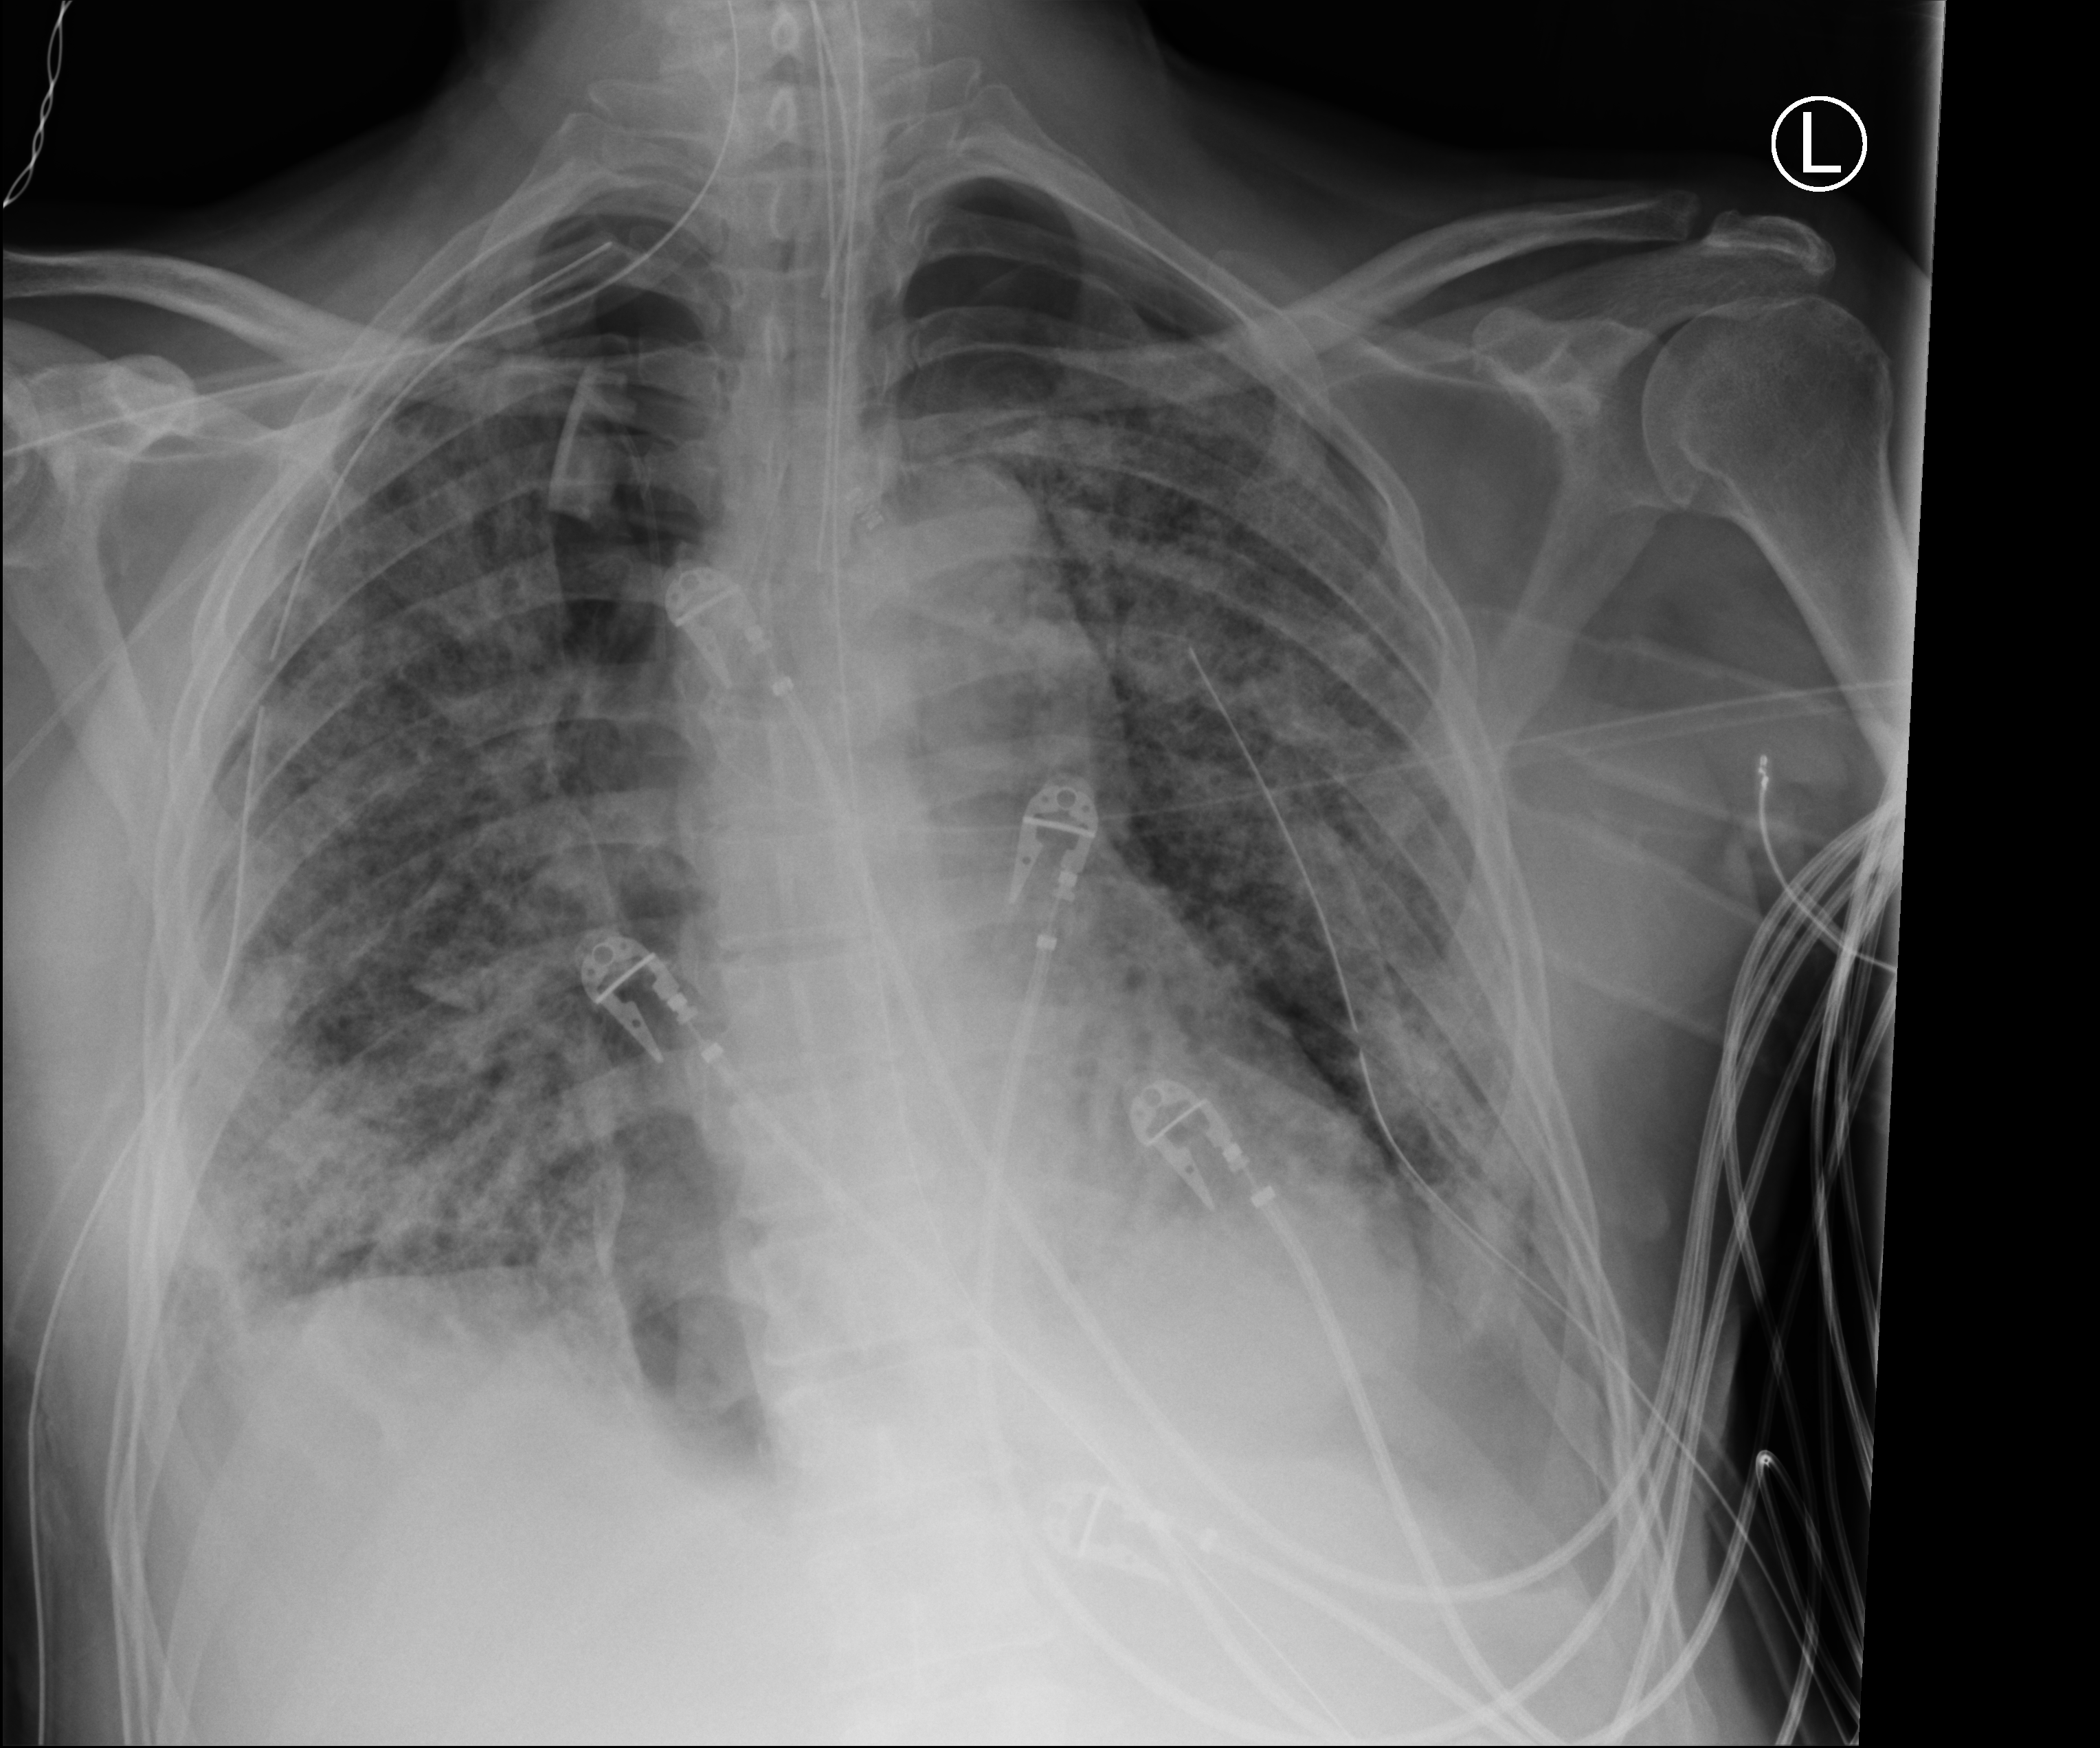
Bedside chest radiograph (computed radiography); anteroposterior (AP) projection. Patient hospitalised with COVID-19; male, aged 60–74 years.
From the hospital-stay record, not from the radiograph (when in the stay this image was taken is not recorded): admitted to intensive care during this hospital stay: yes.